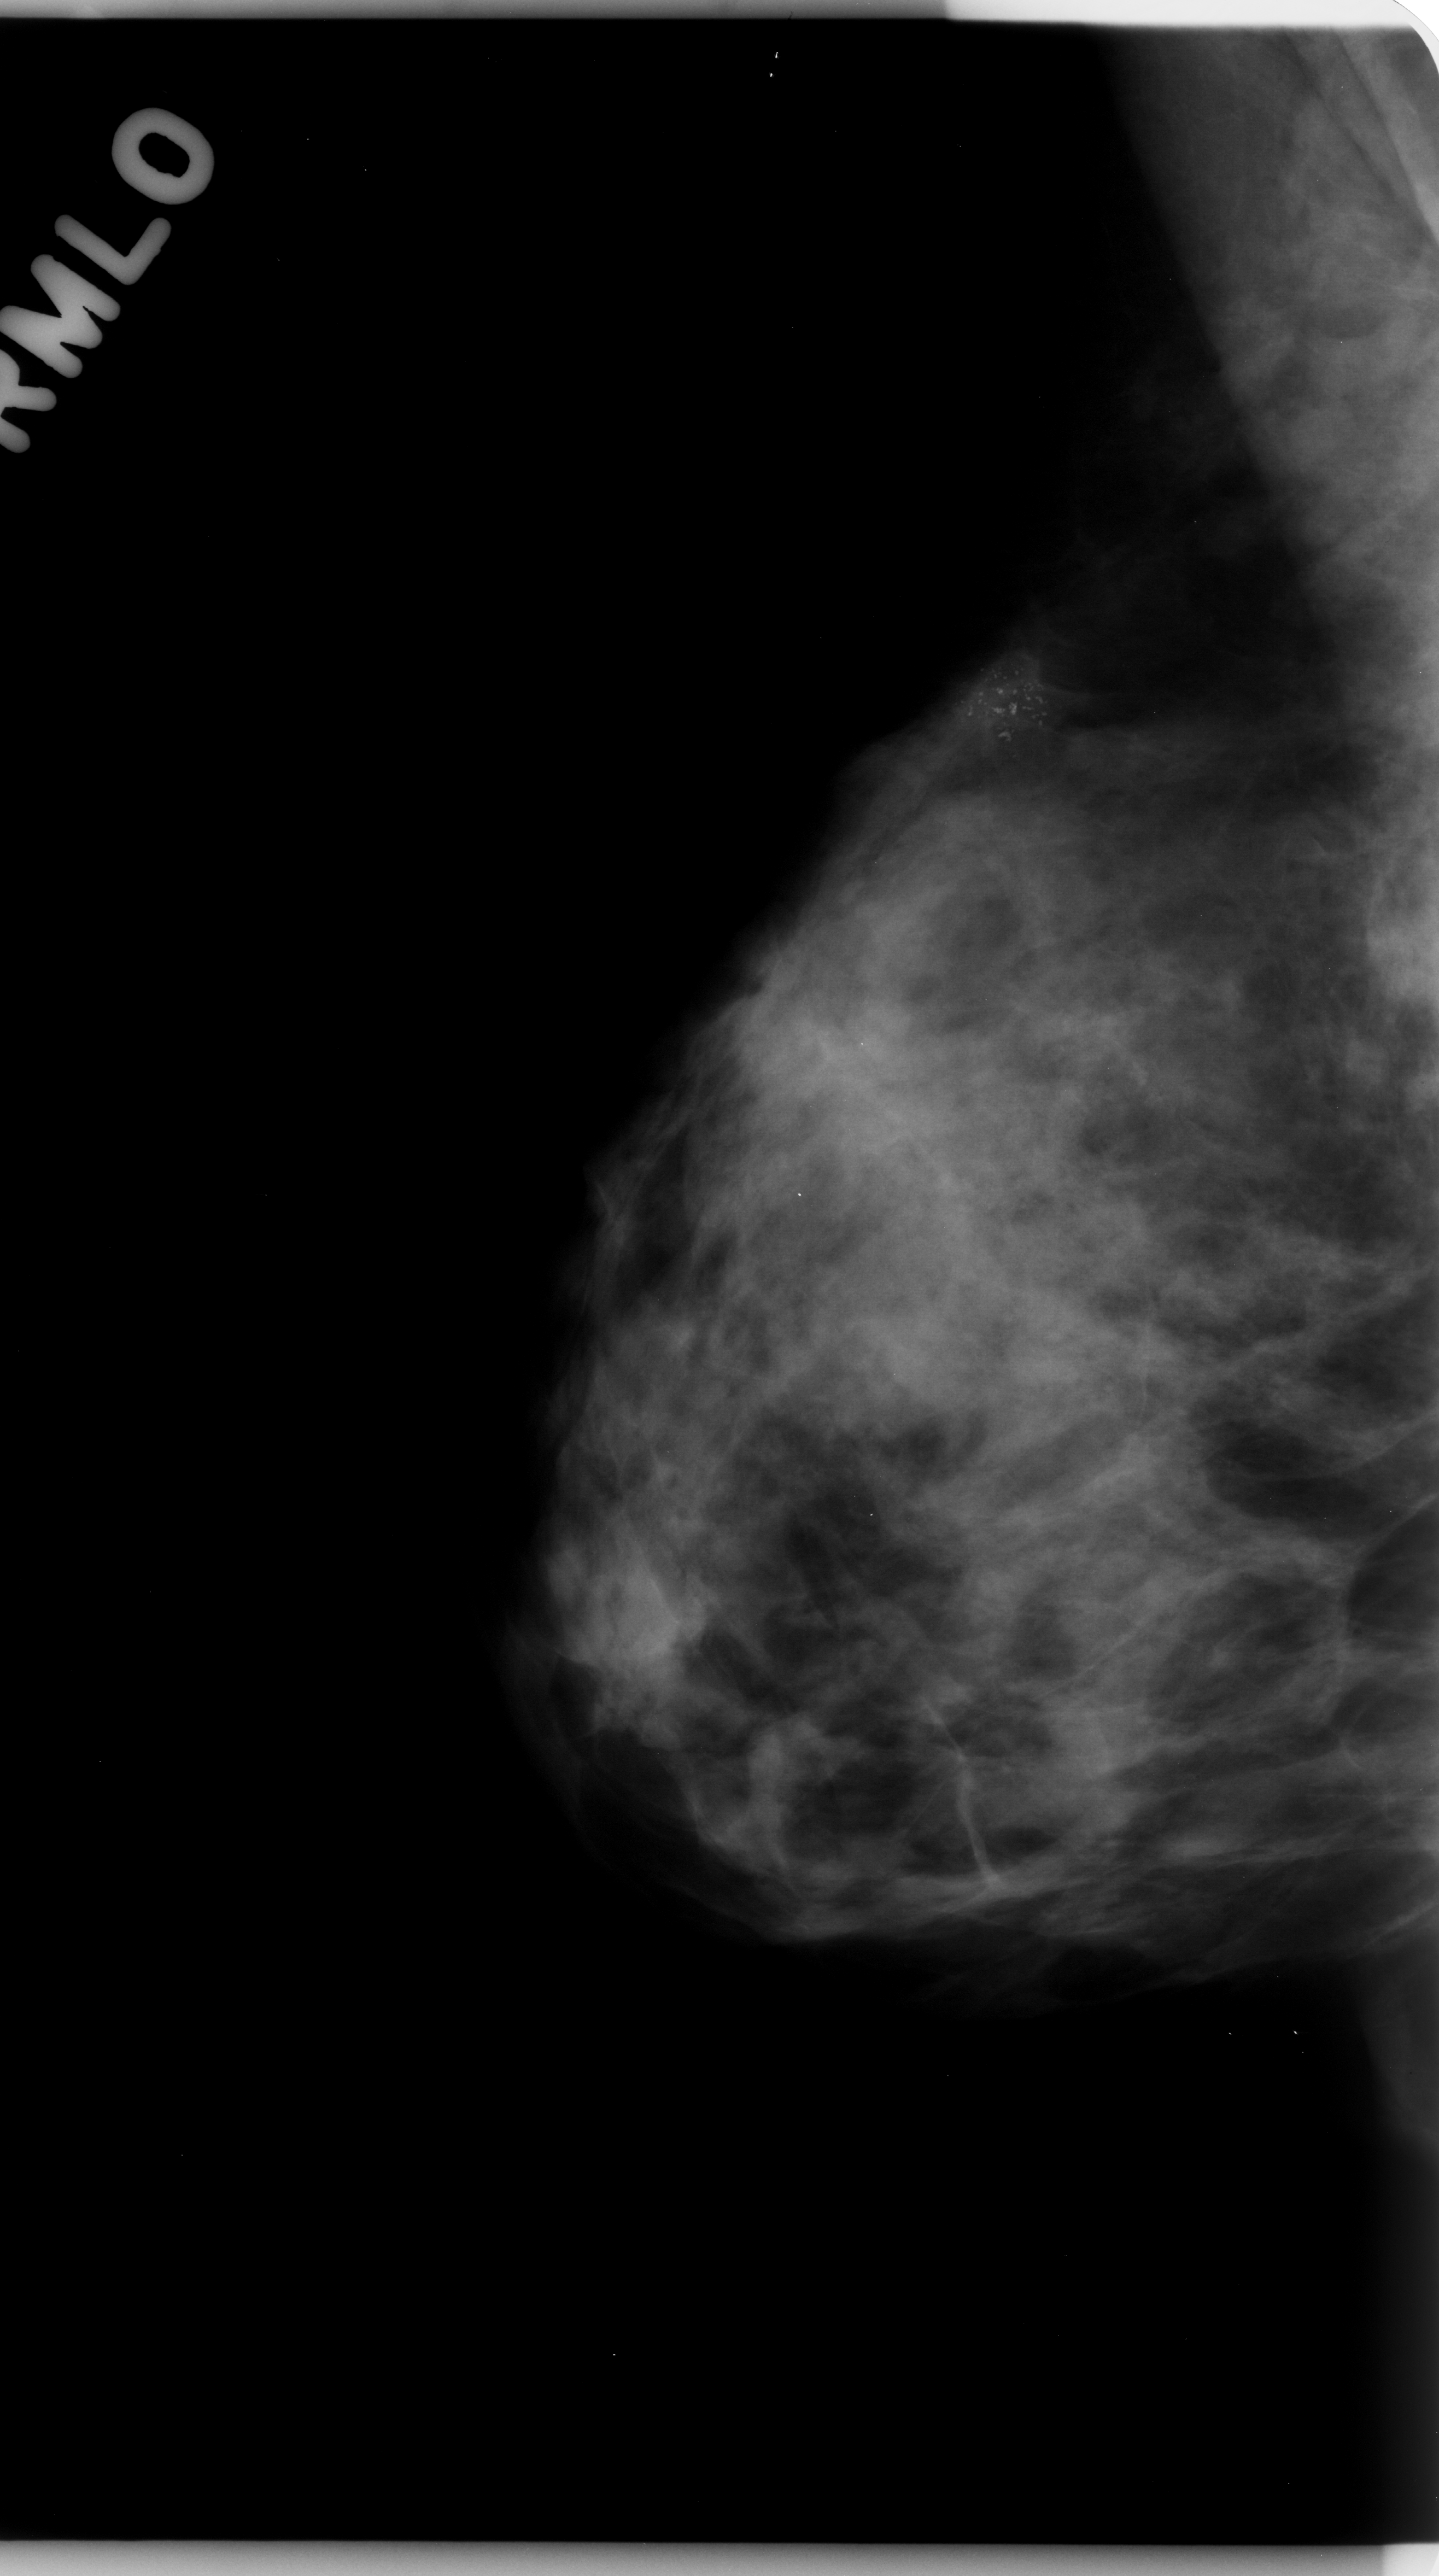
Scanned film-screen mammogram, right breast, MLO view, breast composition: heterogeneously dense (BI-RADS density category 3 of 4).
- Abnormality record for this image: calcifications, morphology pleomorphic, distribution clustered; BI-RADS assessment category 5; subtlety rating 5 on a 1 (subtle) to 5 (obvious) scale; pathology (as recorded): malignant.